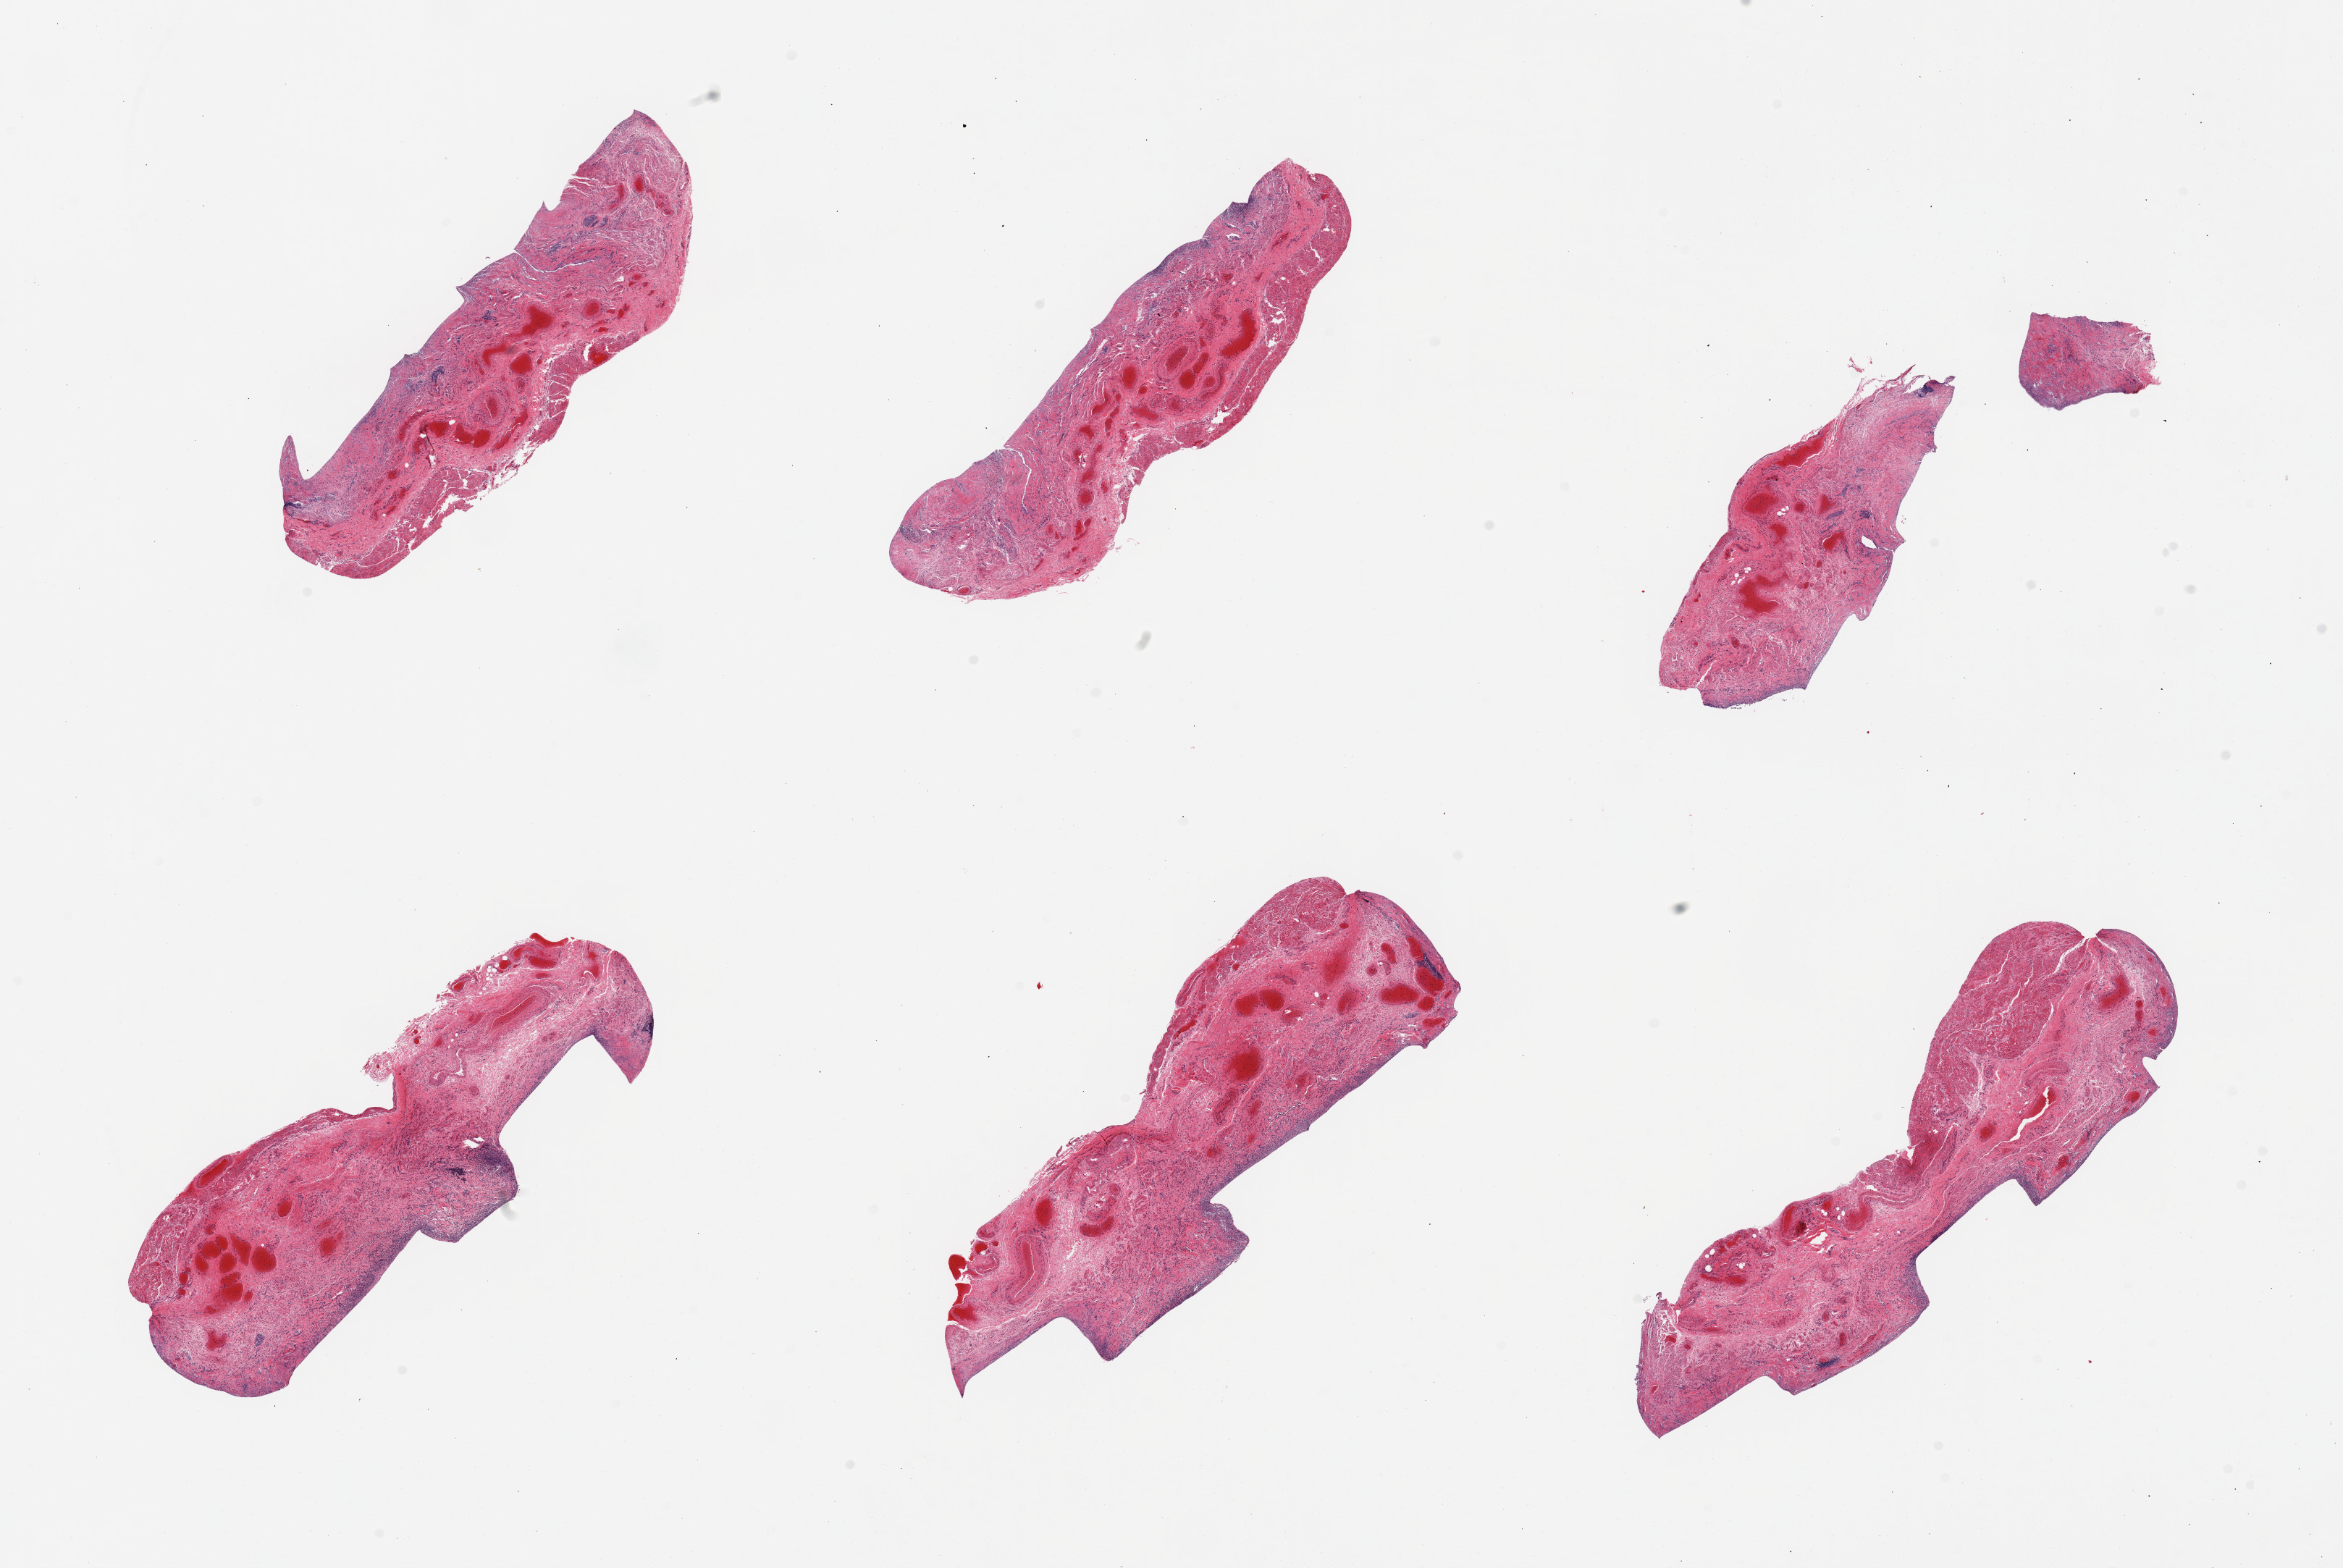
Digitized hematoxylin and eosin (H&E)-stained section — a low-resolution overview of the entire scanned area, about 25.6 x 17.1 mm, PAXgene-fixed paraffin-embedded (PFPE) section, target tissue: esophageal mucous membrane, donor tissue sample. Male donor.
• pathologist's review note for this sample: 6 pieces, remarkably advanced autolysis, mucosa completely sloughed